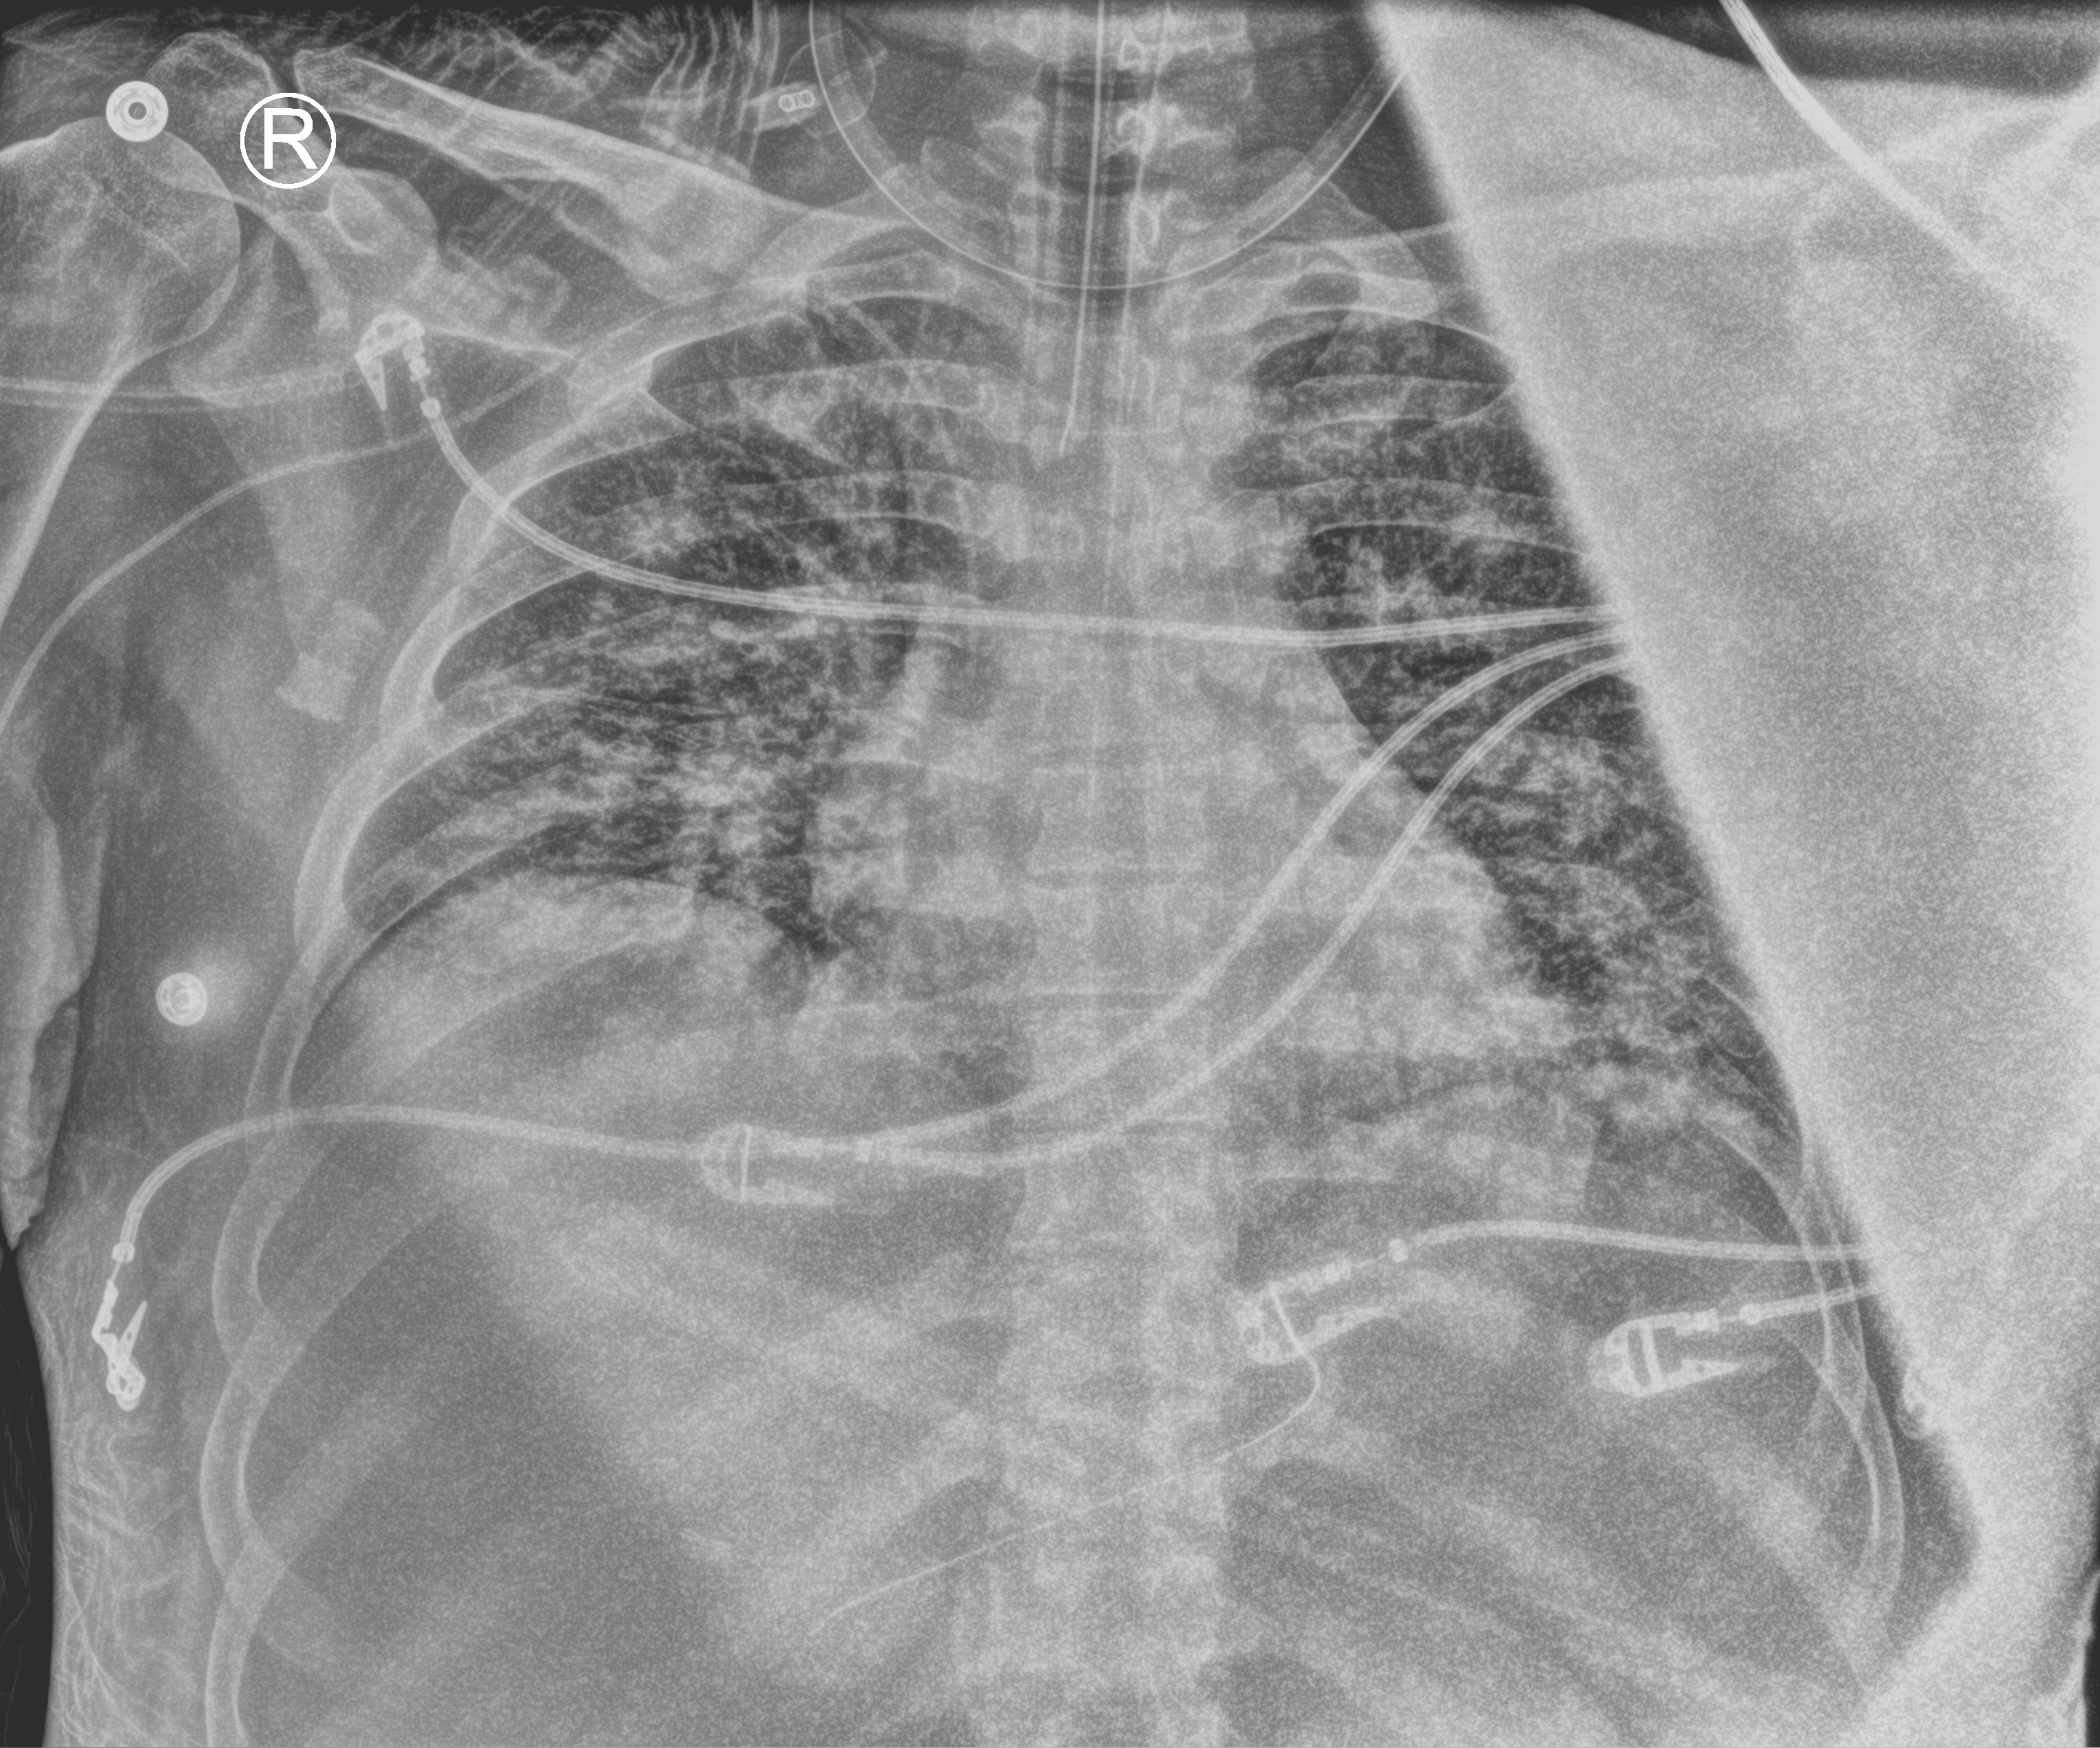
Portable chest radiograph; anteroposterior (AP) projection. Patient hospitalised with COVID-19; male, aged 18–59 years.
Hospital-stay facts (about this admission, not read from this image; timing relative to this image not recorded):
- length of hospital stay: 44 days
- mechanically ventilated during this hospital stay: yes
- admitted to intensive care during this hospital stay: yes